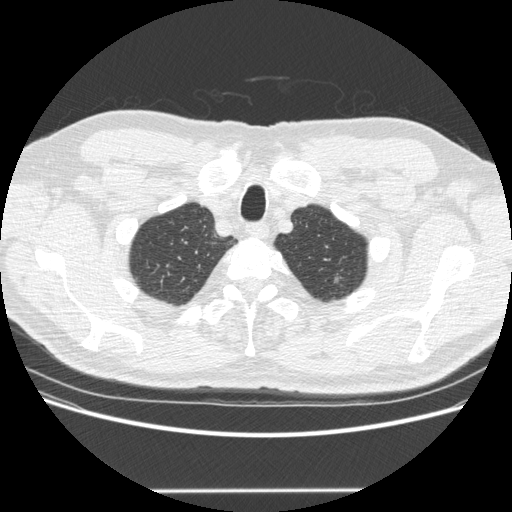
Low-dose screening chest CT, axial slice. Second screening round (one year after baseline). Lung window (W 1500 / L -600 HU). 1.25 mm slice thickness. Standard (soft-tissue) reconstruction kernel (STANDARD). Male participant, aged 69 years at enrolment. Former smoker at enrolment.
Lesion marked by an expert reader, bounding box (x1, y1, x2, y2) in pixels: (313, 264, 346, 294). No non-calcified nodule or mass ≥4 mm was recorded by the screening reader at this exam. Official screen result: negative screen, significant abnormalities not suspicious for lung cancer. Lung cancer was diagnosed 485 days after this screen (after the third annual screen): adenocarcinoma, NOS, left upper lobe, moderately differentiated (G2), stage IA (AJCC 6th edition), 10 mm at pathology.